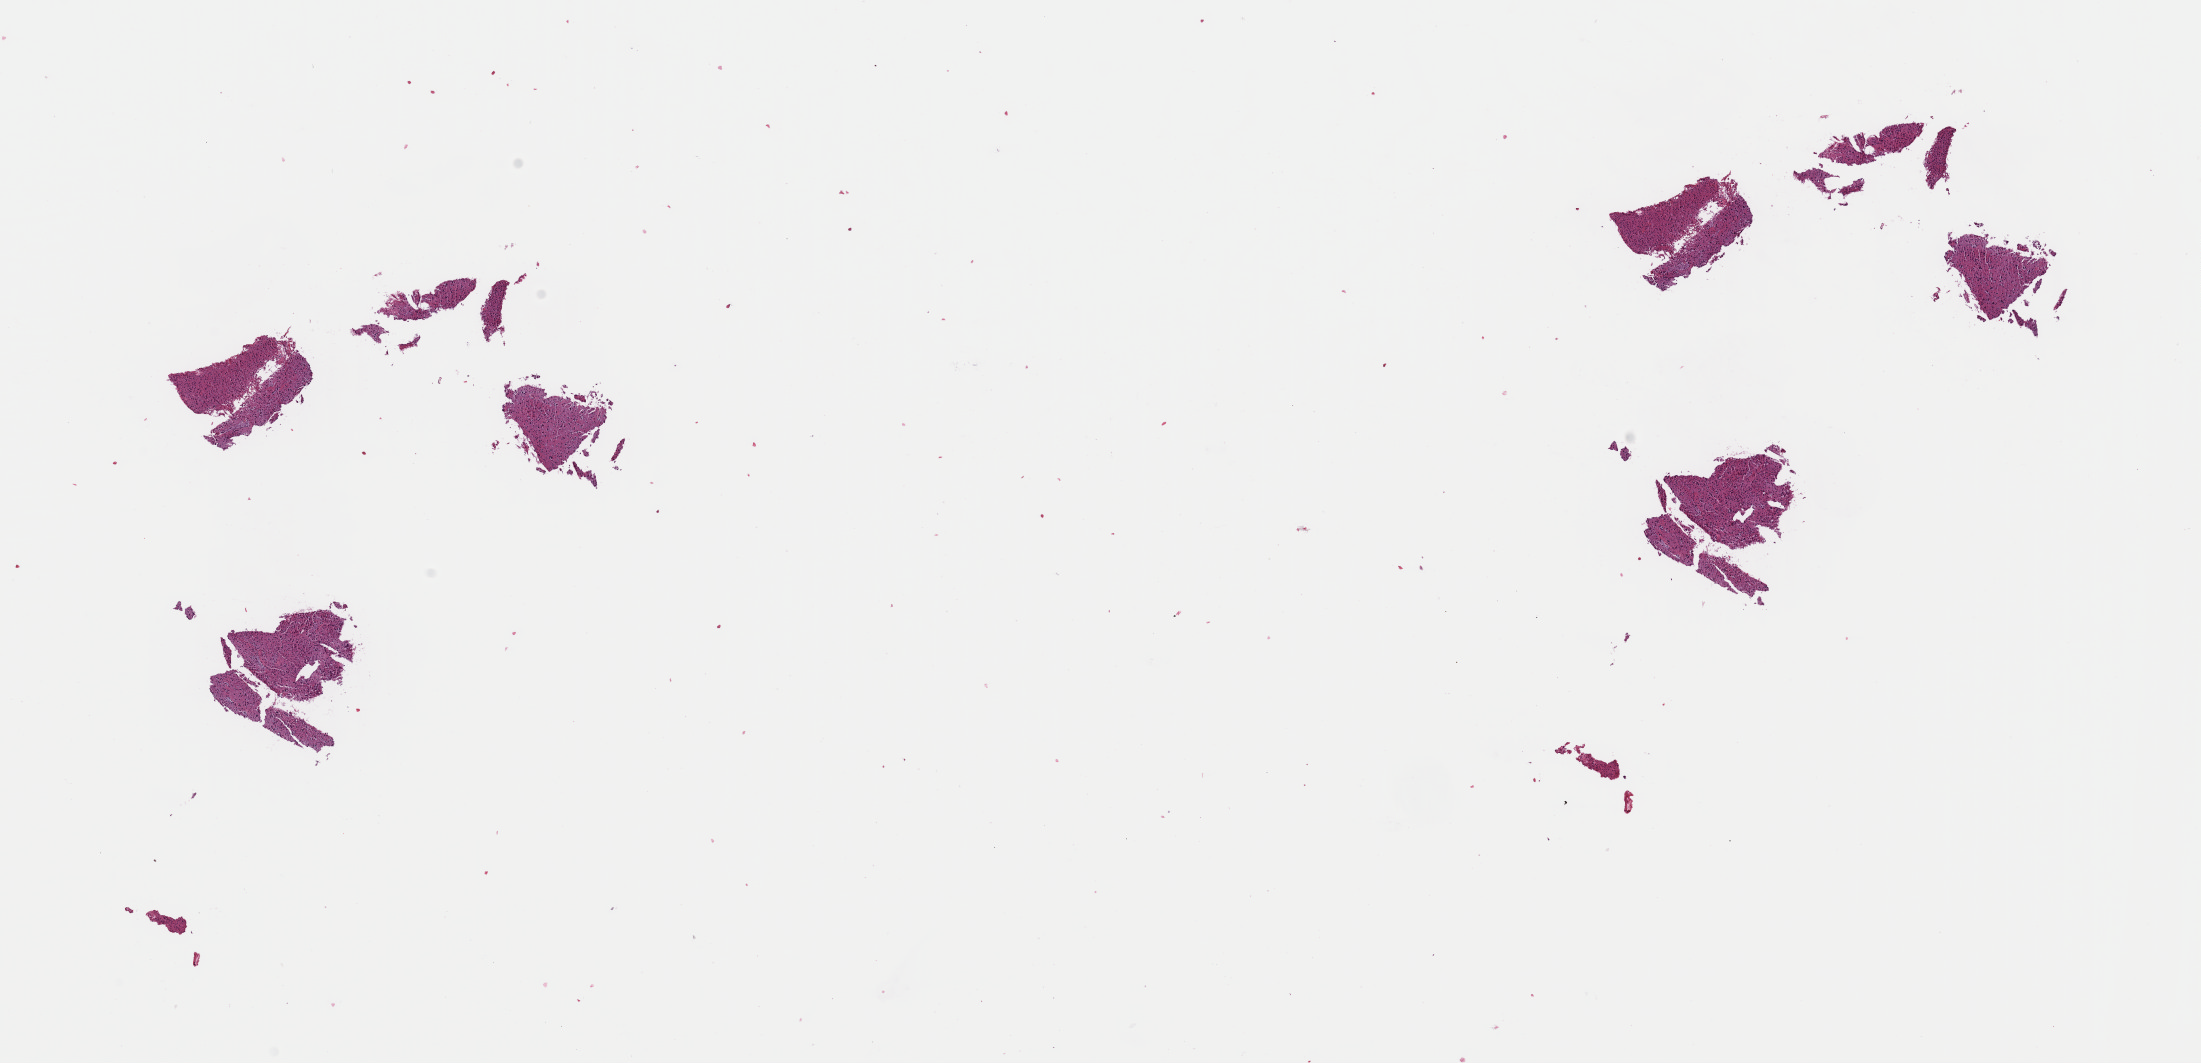
Whole-slide histology image, Hematoxylin and eosin (H&E) stained — low-resolution overview of the scanned area, about 17.4 x 8.4 mm, formalin-fixed paraffin-embedded (FFPE) diagnostic section, primary tumour sample from the brain. Female patient; age at initial diagnosis 44 years. Histologic grade: G2 (moderately differentiated).
- diagnosis: Astrocytoma, NOS (cerebrum)